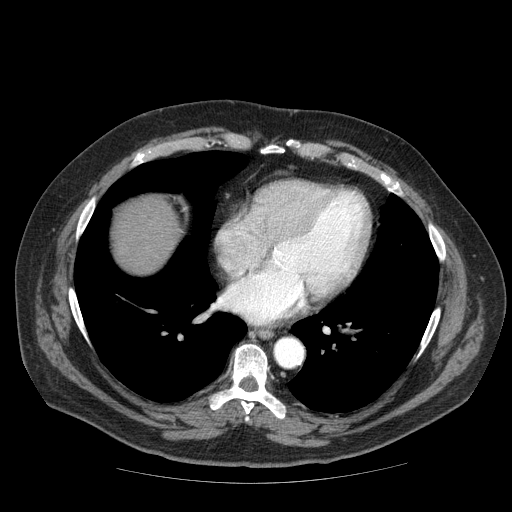
Contrast-enhanced abdominal CT (liver protocol), one axial slice; slice 73 of 85 in the series (ordered by position); reconstruction kernel STANDARD; 120 kVp; soft-tissue window (W 400 / L 40 HU); 512 × 512 image matrix, field of view 420 × 420 mm. Case-level facts recorded for this patient, not image findings: diagnosis: hepatocellular carcinoma (patient treated with transarterial chemoembolisation; whether this scan precedes or follows treatment is not stated here); TNM stage (as recorded): Stage-IIIA; Child-Pugh class: A; tumour size: 7 cm.
Structures marked on this image (semi-automatic segmentation, software-assisted and operator-edited):
- liver parenchyma outside the tumour (the mass and vessels are separate outlines, so this box may not span the whole liver): bounding box [x1, y1, x2, y2] px = [112, 196, 180, 272]